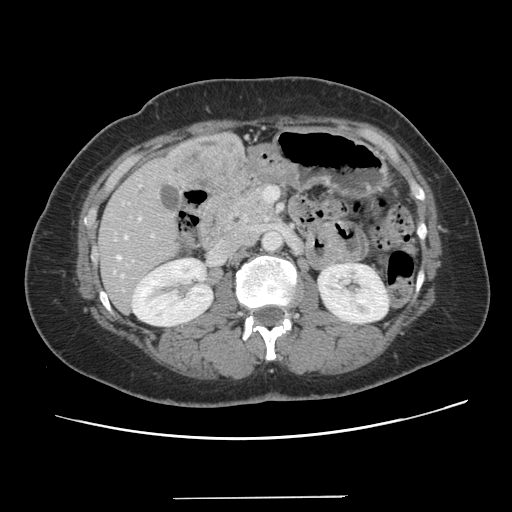
Contrast-enhanced abdominal CT, one axial slice; slice 54 of 141 in the series (ordered by position); intravenous contrast given; soft-tissue window (W 400 / L 40 HU); 512 × 512 image matrix, field of view 366 × 366 mm. Female patient, age 53 years. Case-level facts recorded for this patient, not image findings: diagnosis: colorectal cancer liver metastases, imaged before liver resection; multiple liver metastases: no; largest metastasis: 14.5 cm; disease in both lobes: yes.
Structures marked on this image (expert manual segmentation):
- hepatic veins: bounding box <116,236,126,260> (left, top, right, bottom; pixels)
- liver: <98,134,244,312>
- planned liver remnant (the part of the liver to remain after resection): <97,218,180,312>
- portal vein (with intrahepatic branches): <139,218,153,236>
- liver metastasis: <174,138,243,185>